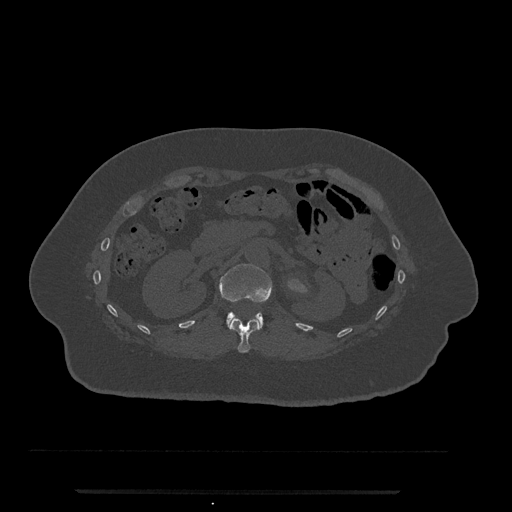
CT including the spine, one axial slice; slice 135 of 797 in the series (ordered by position); reconstruction kernel Br40s/3; 120 kVp; bone window (W 1800 / L 400 HU); 0.5 mm slice thickness; 512 × 512 image matrix. Female patient, age 51 years. From the clinical record (not read from this slice): primary cancer: neuro; vertebrae with lytic lesions (as recorded): T8.
Outlined on this slice (semi-automatically segmented with operator editing):
- L1 vertebra: box from (x=219, y=264) to (x=272, y=329) px
- T12 vertebra: (x=229, y=317)–(x=259, y=353)